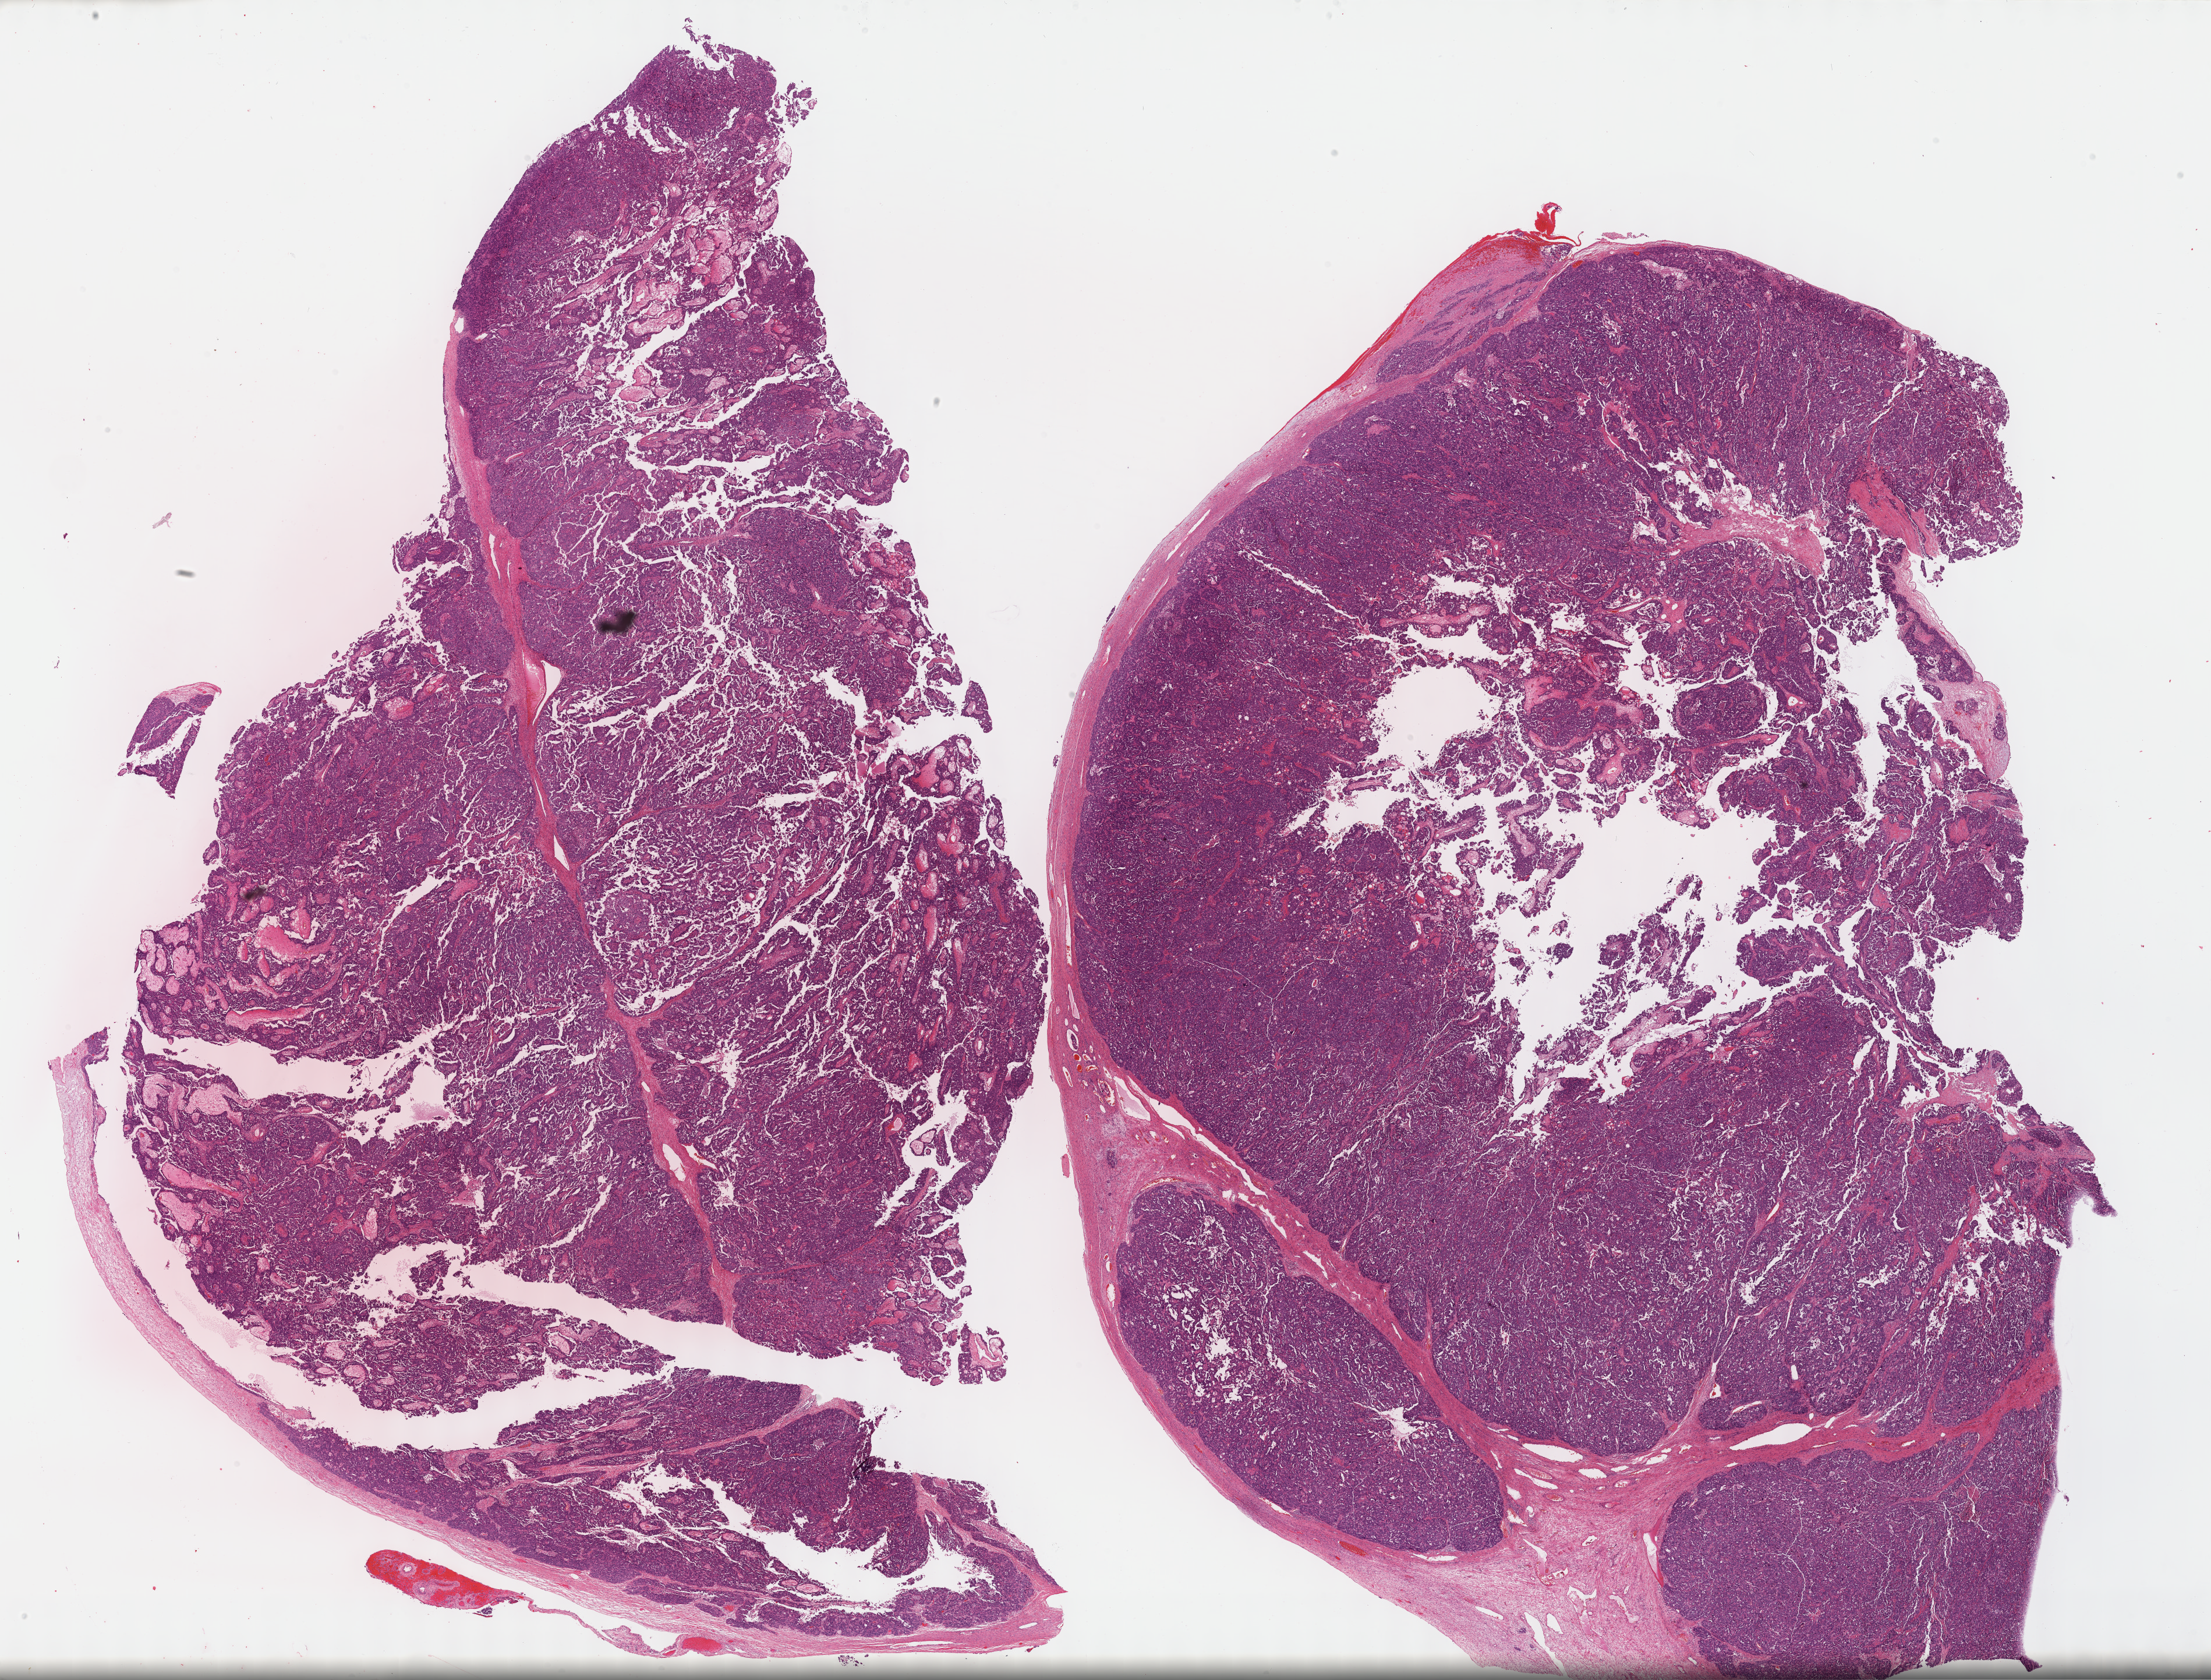
Hematoxylin and eosin (H&E) stained whole-slide image — a low-resolution overview of the entire scanned area, about 30.7 x 23.3 mm. Formalin-fixed paraffin-embedded (FFPE) diagnostic section. Ovary, primary tumour sample. Female patient; age at initial diagnosis 42 years. Histologic grade: G3 (poorly differentiated).
Laterality: left. FIGO stage: IIIC. Pathologic diagnosis: Serous cystadenocarcinoma, NOS.